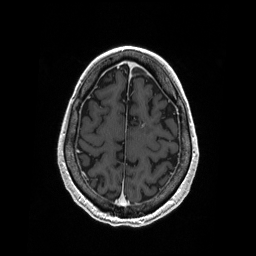
Brain MRI from a brain-tumour surgery series, one axial slice. Slice 58 of 208 in the series (ordered by position). T1-weighted post-contrast. 1 mm slice thickness. 256 × 256 image matrix, field of view 256 × 256 mm. Case-level facts recorded for this patient, not image findings: histopathology: Primary diffuse large B-cell lymphoma.
Structures marked on this image (outlined manually by an expert reader):
- tumour: box from (x=141, y=124) to (x=145, y=128) px